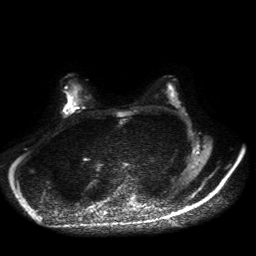
Breast MRI, one axial slice; diffusion-weighted series; image 2 of 4 stored at this slice position (different b-values; order by instance number); 1.5 T; 256 × 256 image matrix. Female patient.
Annotated regions visible in this slice (outlined manually by an expert reader):
- tumour on diffusion-weighted imaging: bounding box (x1, y1, x2, y2) in pixels: (63, 106, 71, 113)